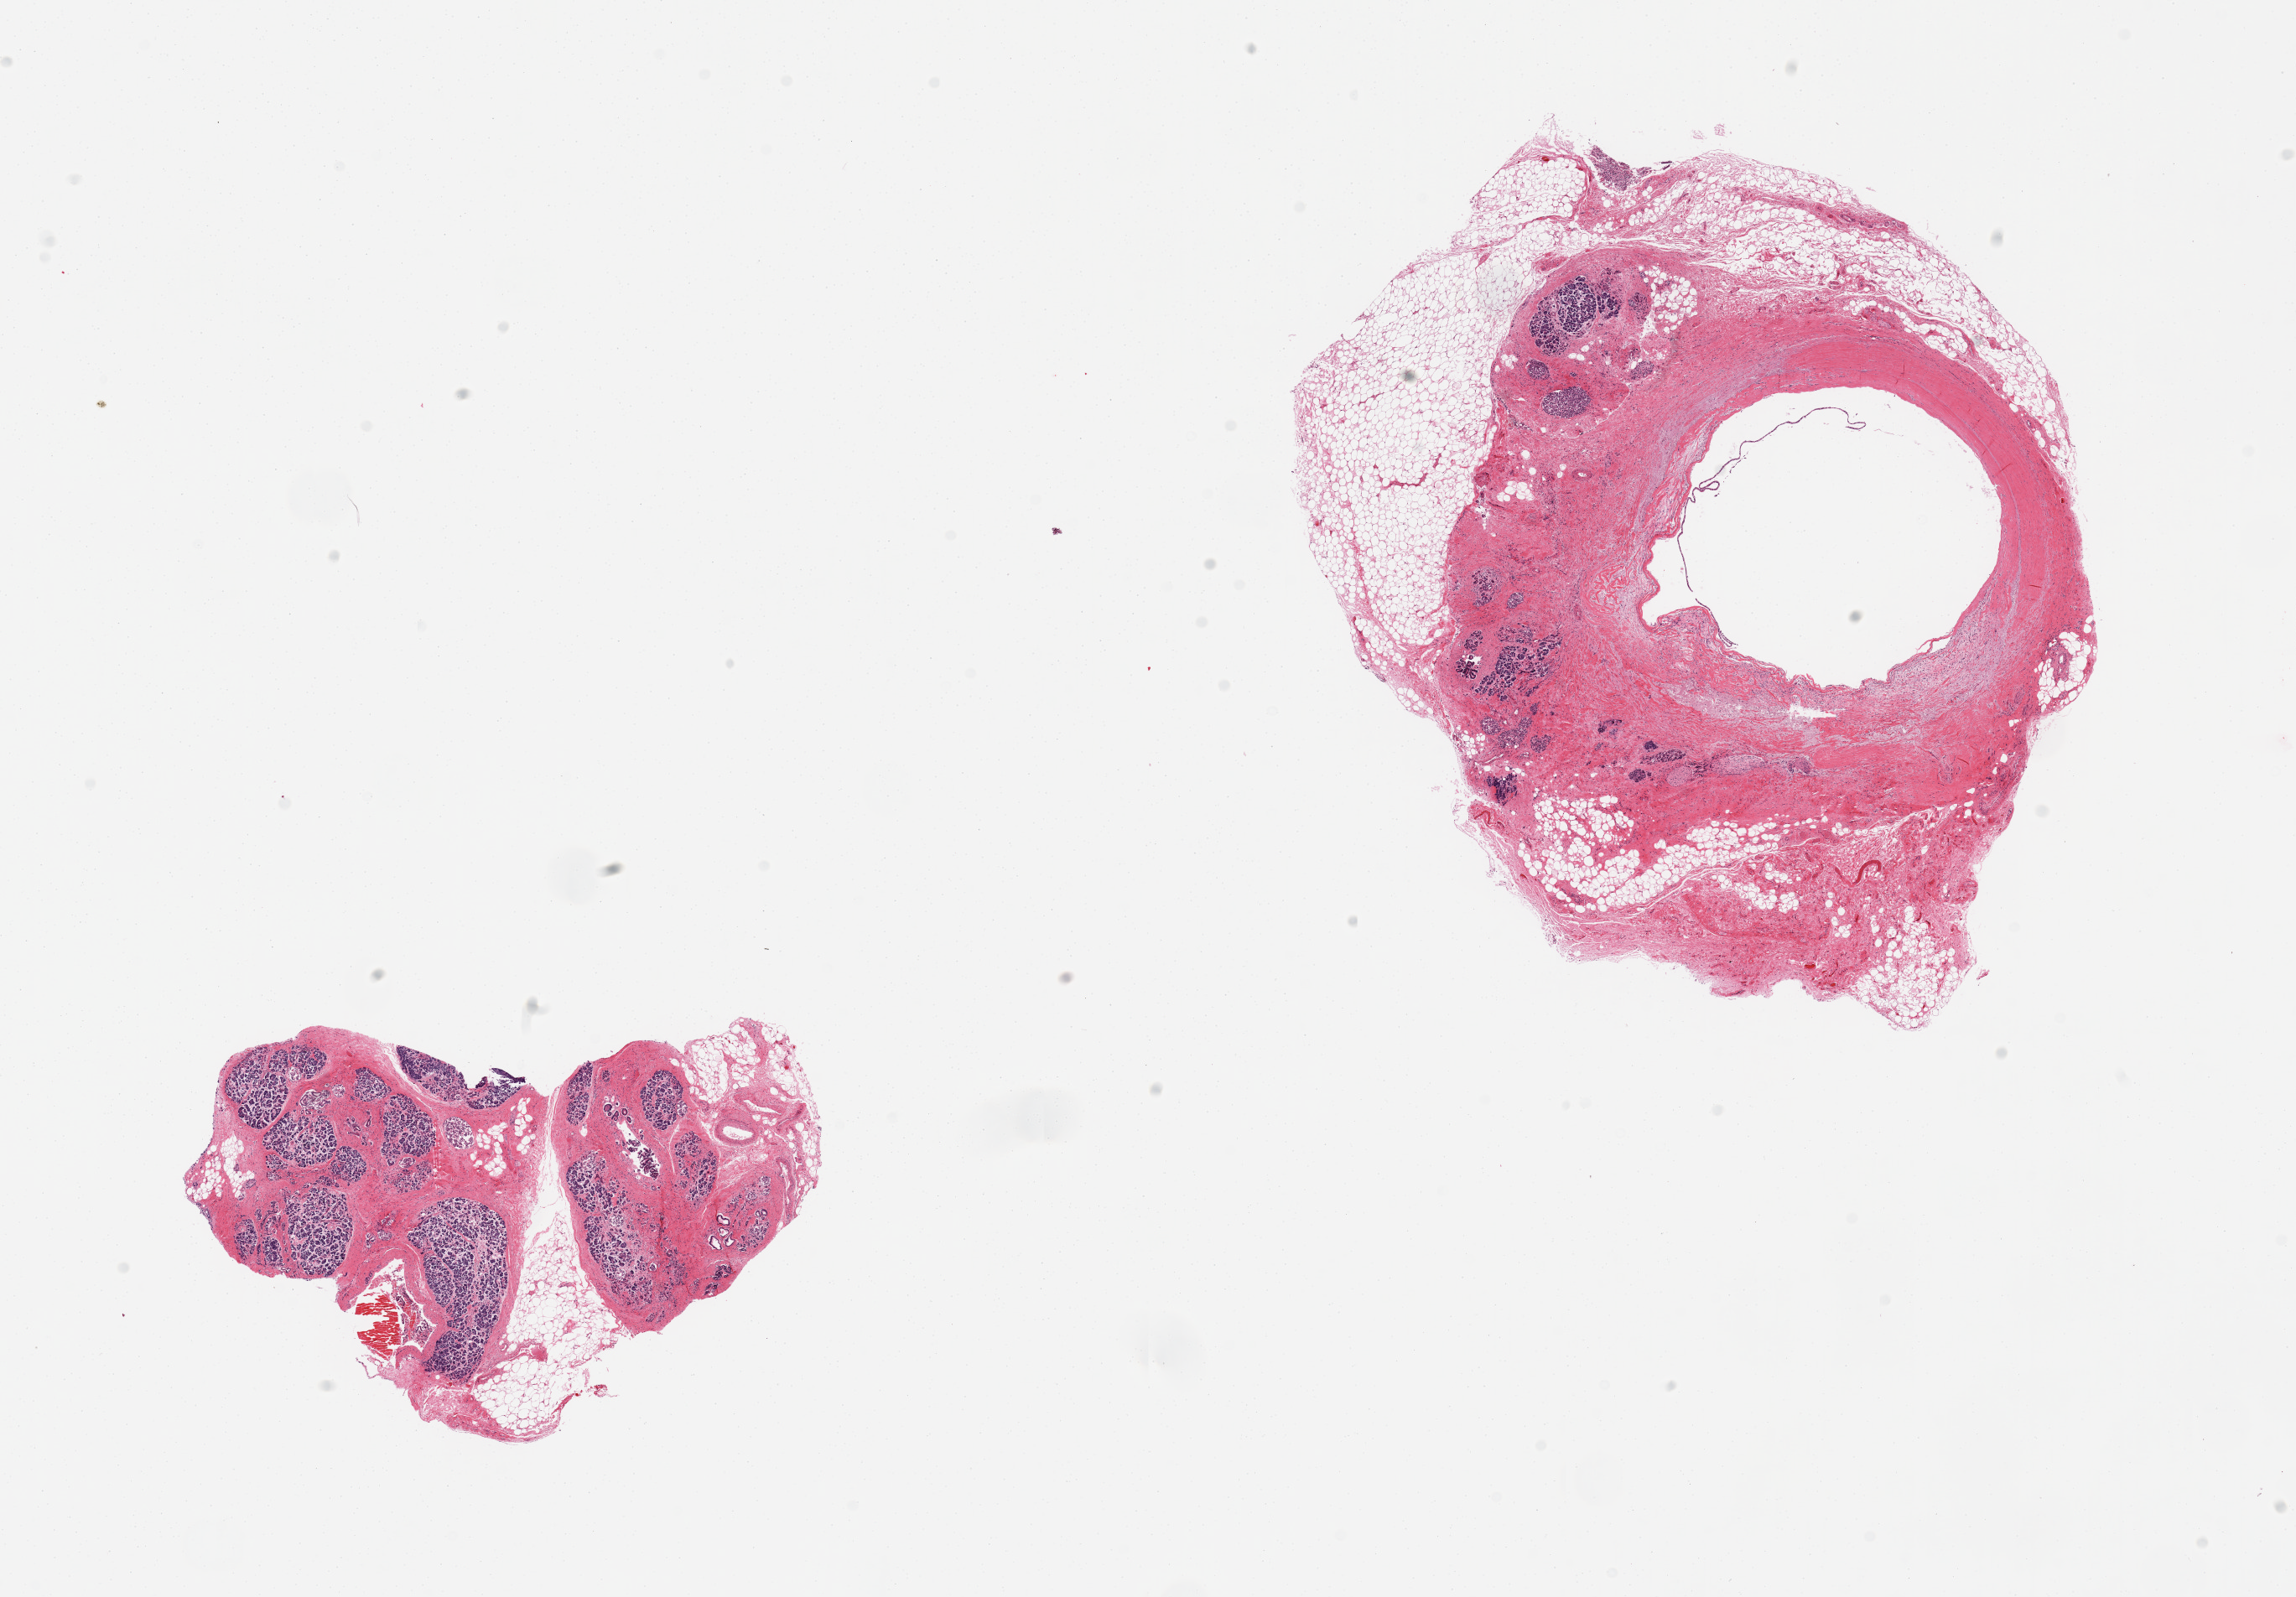
Hematoxylin and eosin (H&E) whole-slide image, shown as a low-resolution overview of the whole scanned area (about 21.7 x 15.1 mm); PAXgene-fixed paraffin-embedded (PFPE) section; sampled site (target tissue): pancreas; tissue donor sample. Male donor.
- reviewer comment on this tissue sample: 2 pieces, fibrosis and atrophy, larger piece is predominantly fat, fibrosis, and cyst with only ~5% parenchyma